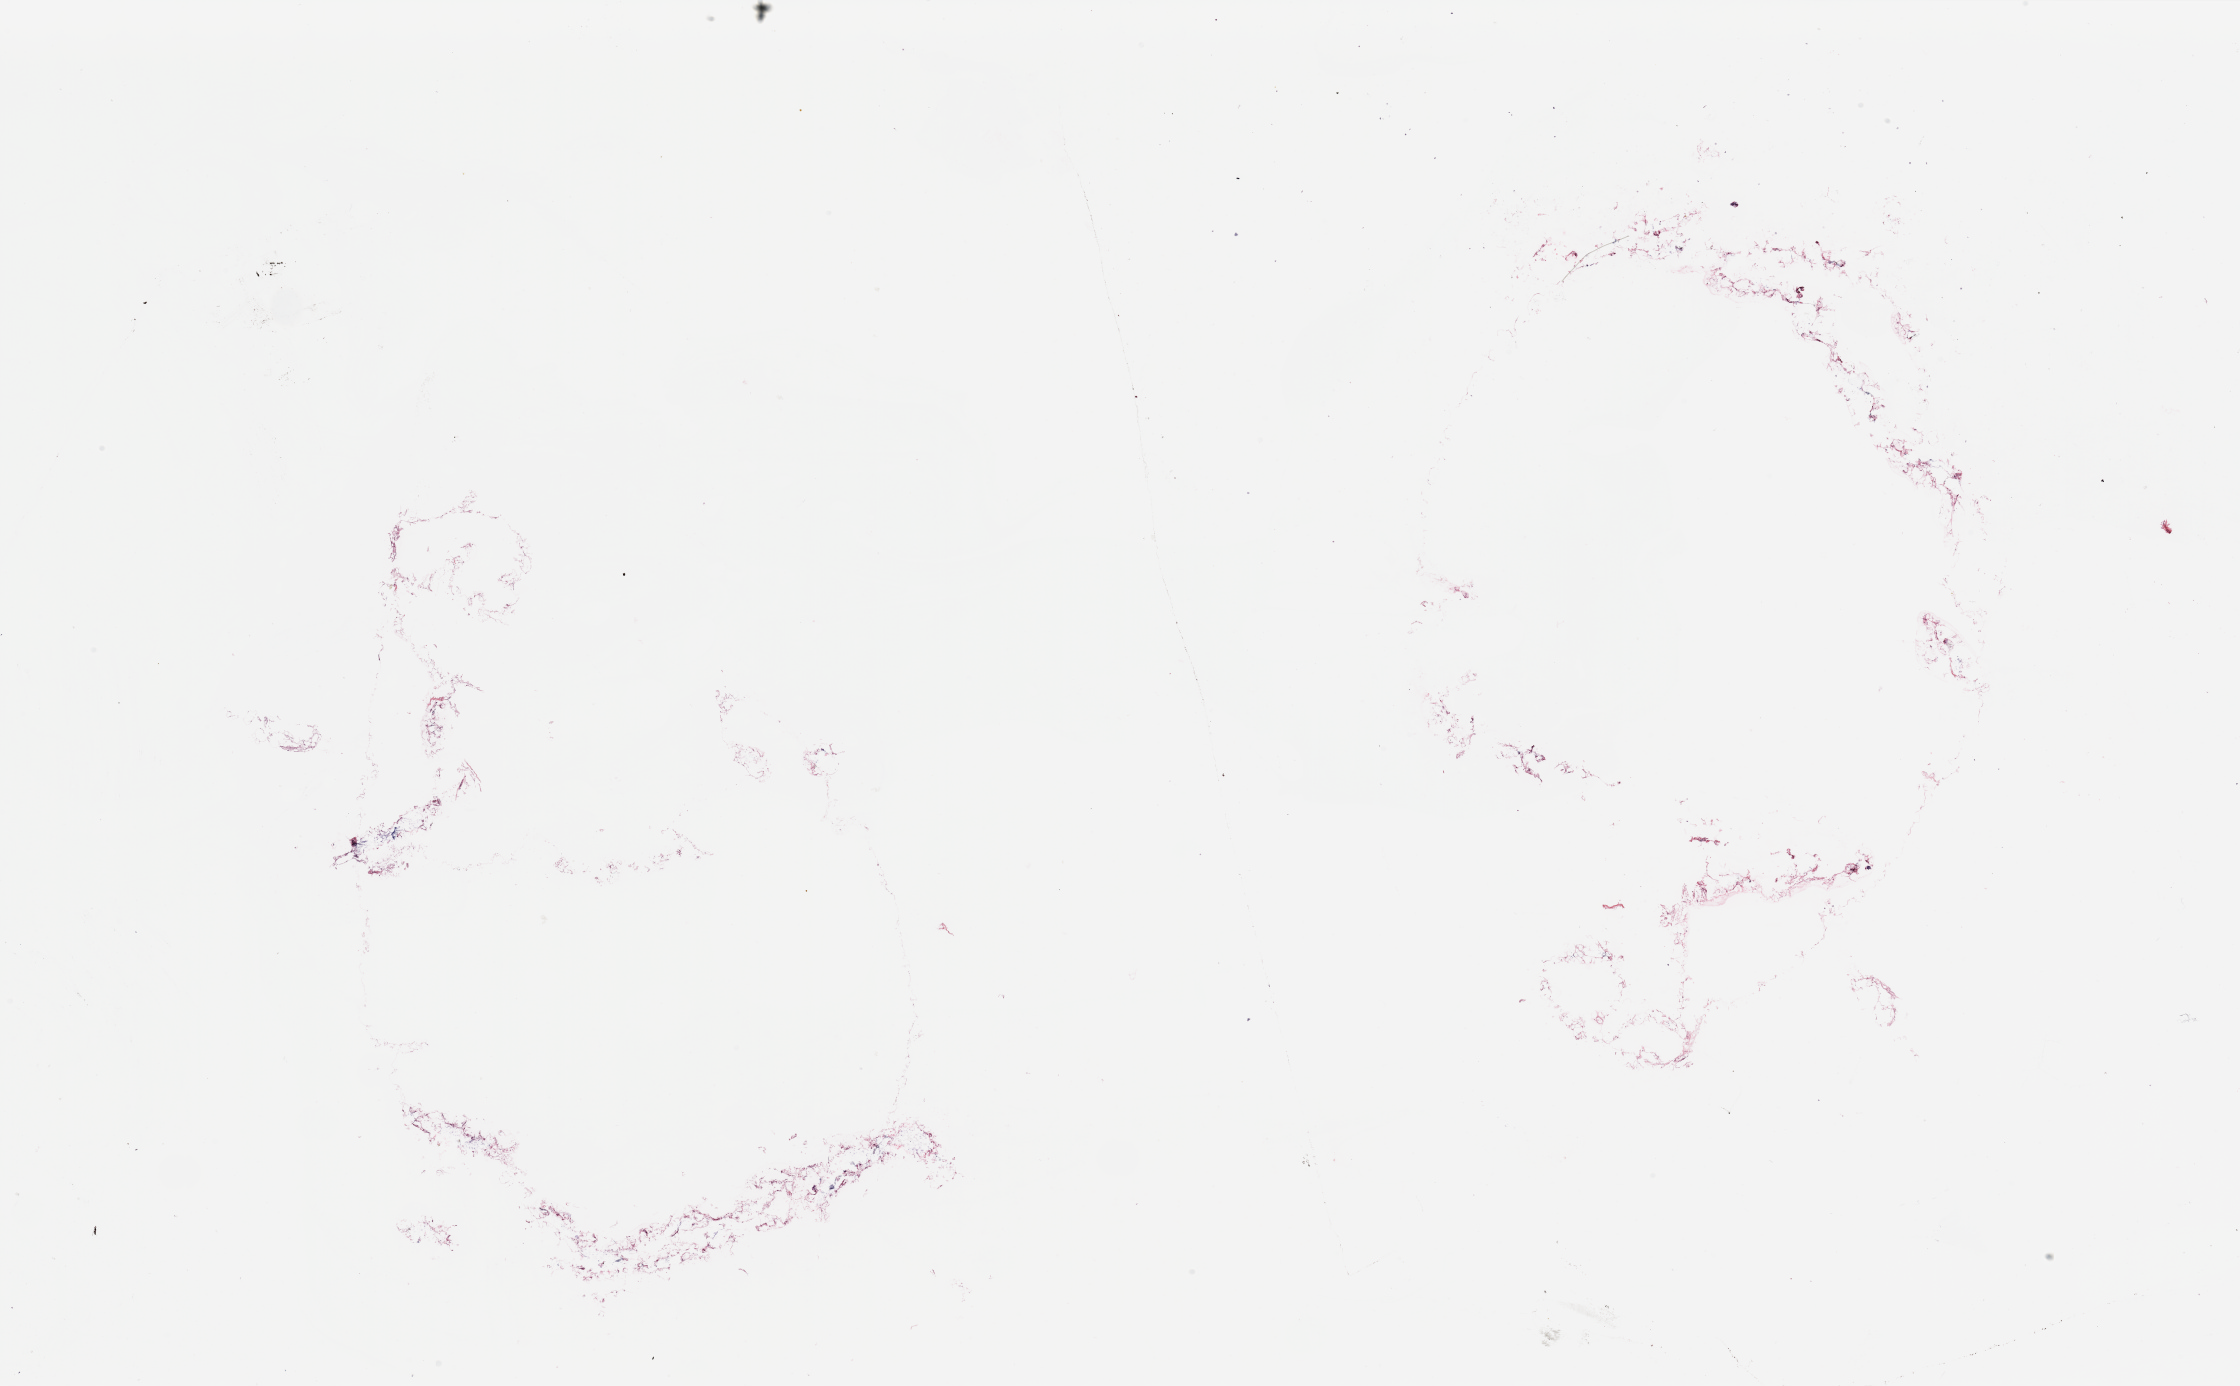
Digitized H&E-stained tissue section (whole slide), whole scanned area (about 35.4 x 21.9 mm, from a 20x scan) shown as a low-resolution overview; breast, tumour tissue. Female, 40 y/o.
Histologic diagnosis: Infiltrating duct carcinoma, NOS. AJCC pathologic stage: IIB.